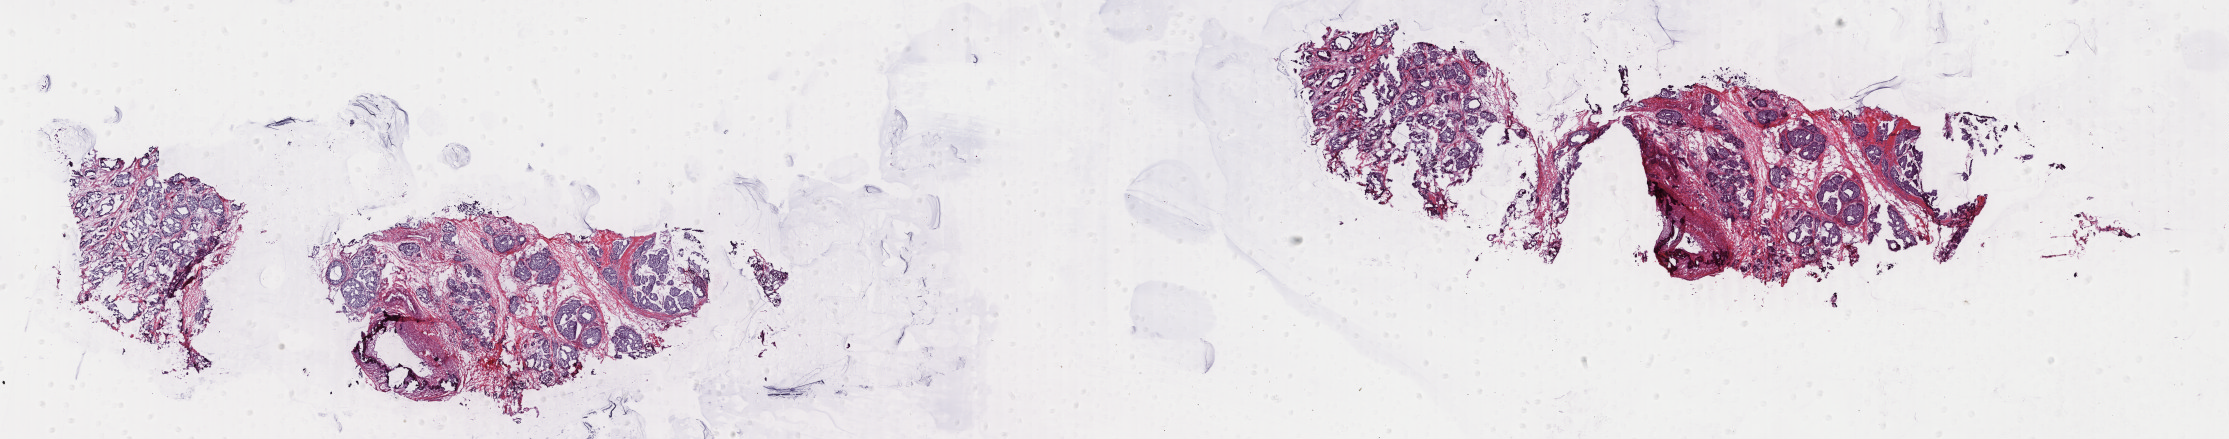
Hematoxylin and eosin (H&E) stained whole-slide image, low-resolution overview of the scanned area, about 35.5 x 7.0 mm (acquisition: 40x scan); frozen section from the bottom of the tissue portion; breast, primary tumour sample. Female patient; age at initial diagnosis 73 years. Pathologist review of this section (percent, as recorded): tumour cells 65%, tumour nuclei 70%.
Pathologic diagnosis: Infiltrating duct carcinoma, NOS.